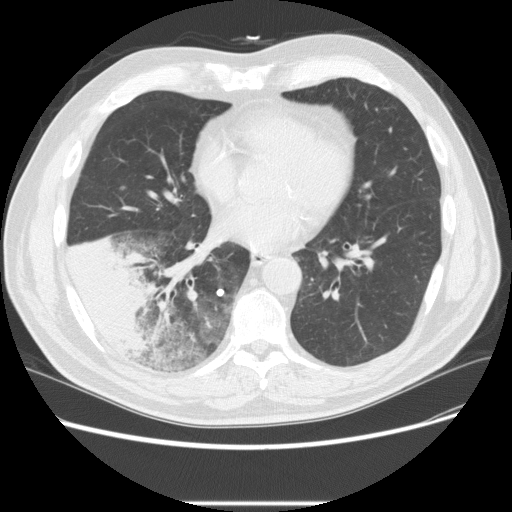
Low-dose screening chest CT, one axial slice. Slice 97 of 233 in the series (ordered by position). Lung window (W 1500 / L -600 HU). 2.5 mm slice thickness. 512 × 512 image matrix, field of view 380 × 380 mm.
Outlined on this slice (manually delineated by an expert):
- lesion 3 (tumor, lower lobe of right lung): box from (x=68, y=235) to (x=159, y=361) px